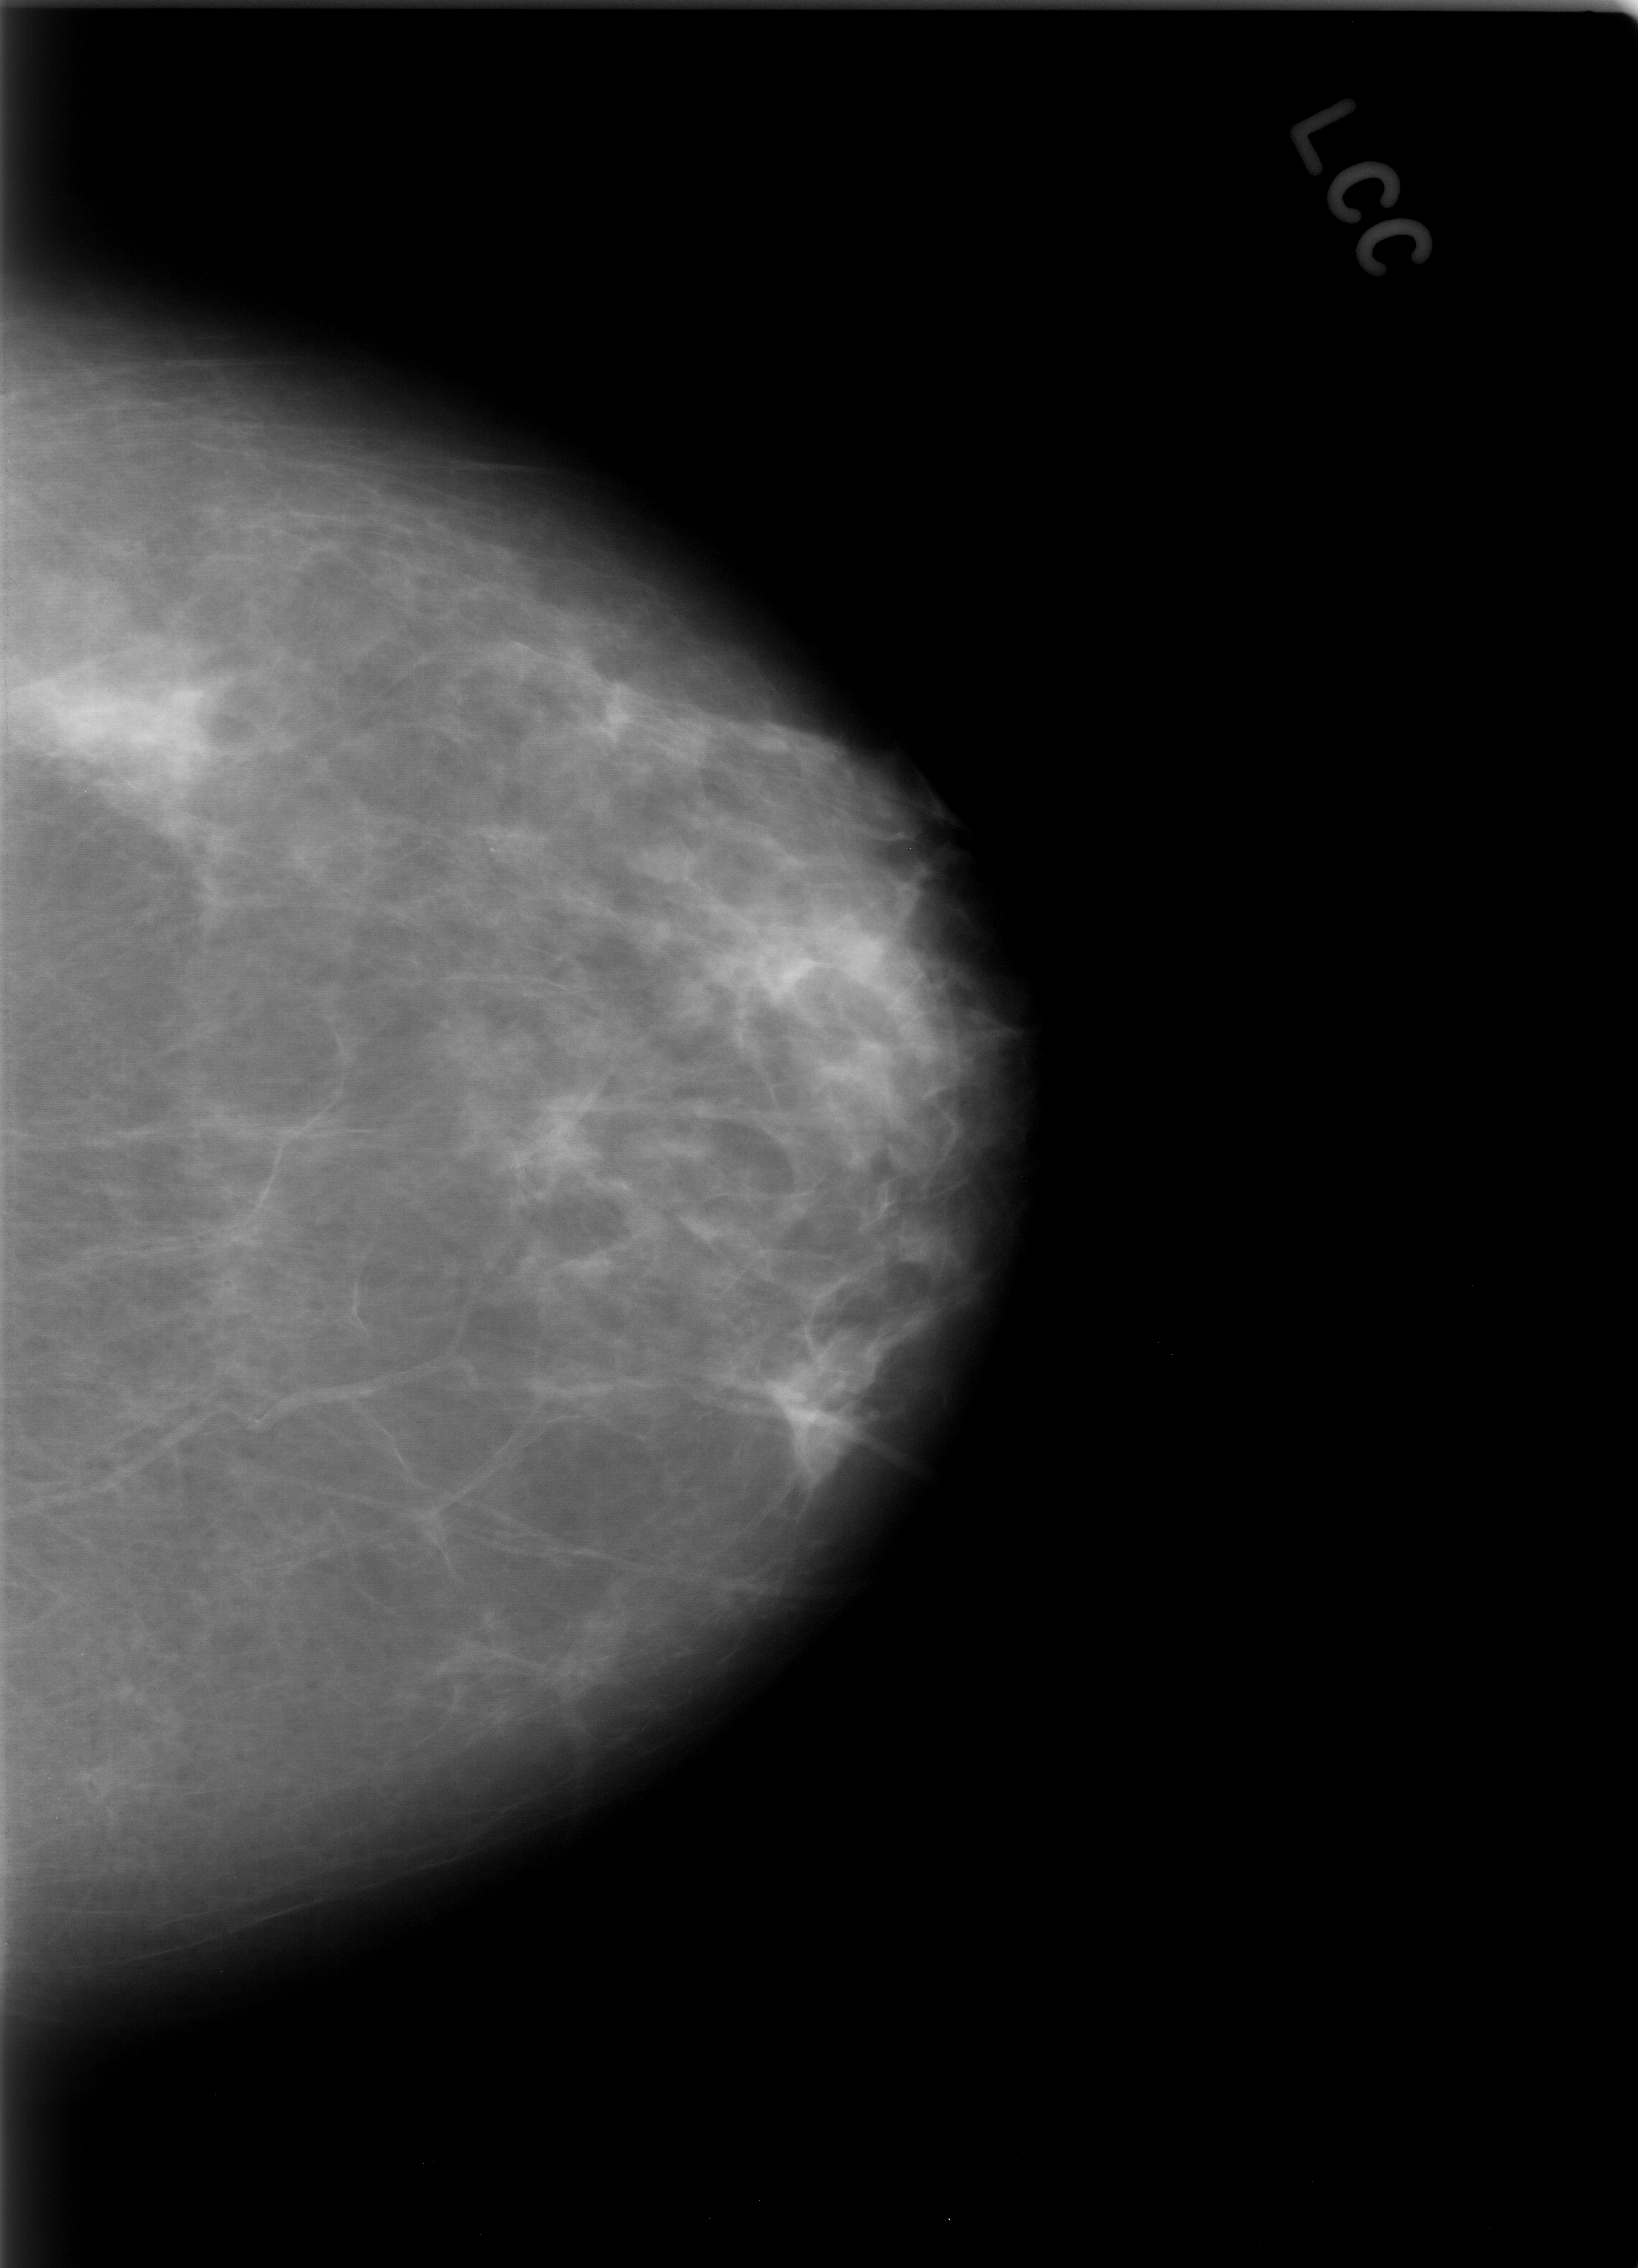
Digitized screen-film mammogram, left breast, craniocaudal (CC) view, breast composition: scattered fibroglandular densities (BI-RADS density category 2 of 4).
Finding: calcifications, morphology pleomorphic, distribution clustered; BI-RADS assessment category 4; subtlety rating 4 on a 1 (subtle) to 5 (obvious) scale; pathology result (as recorded, not read from the image): benign.